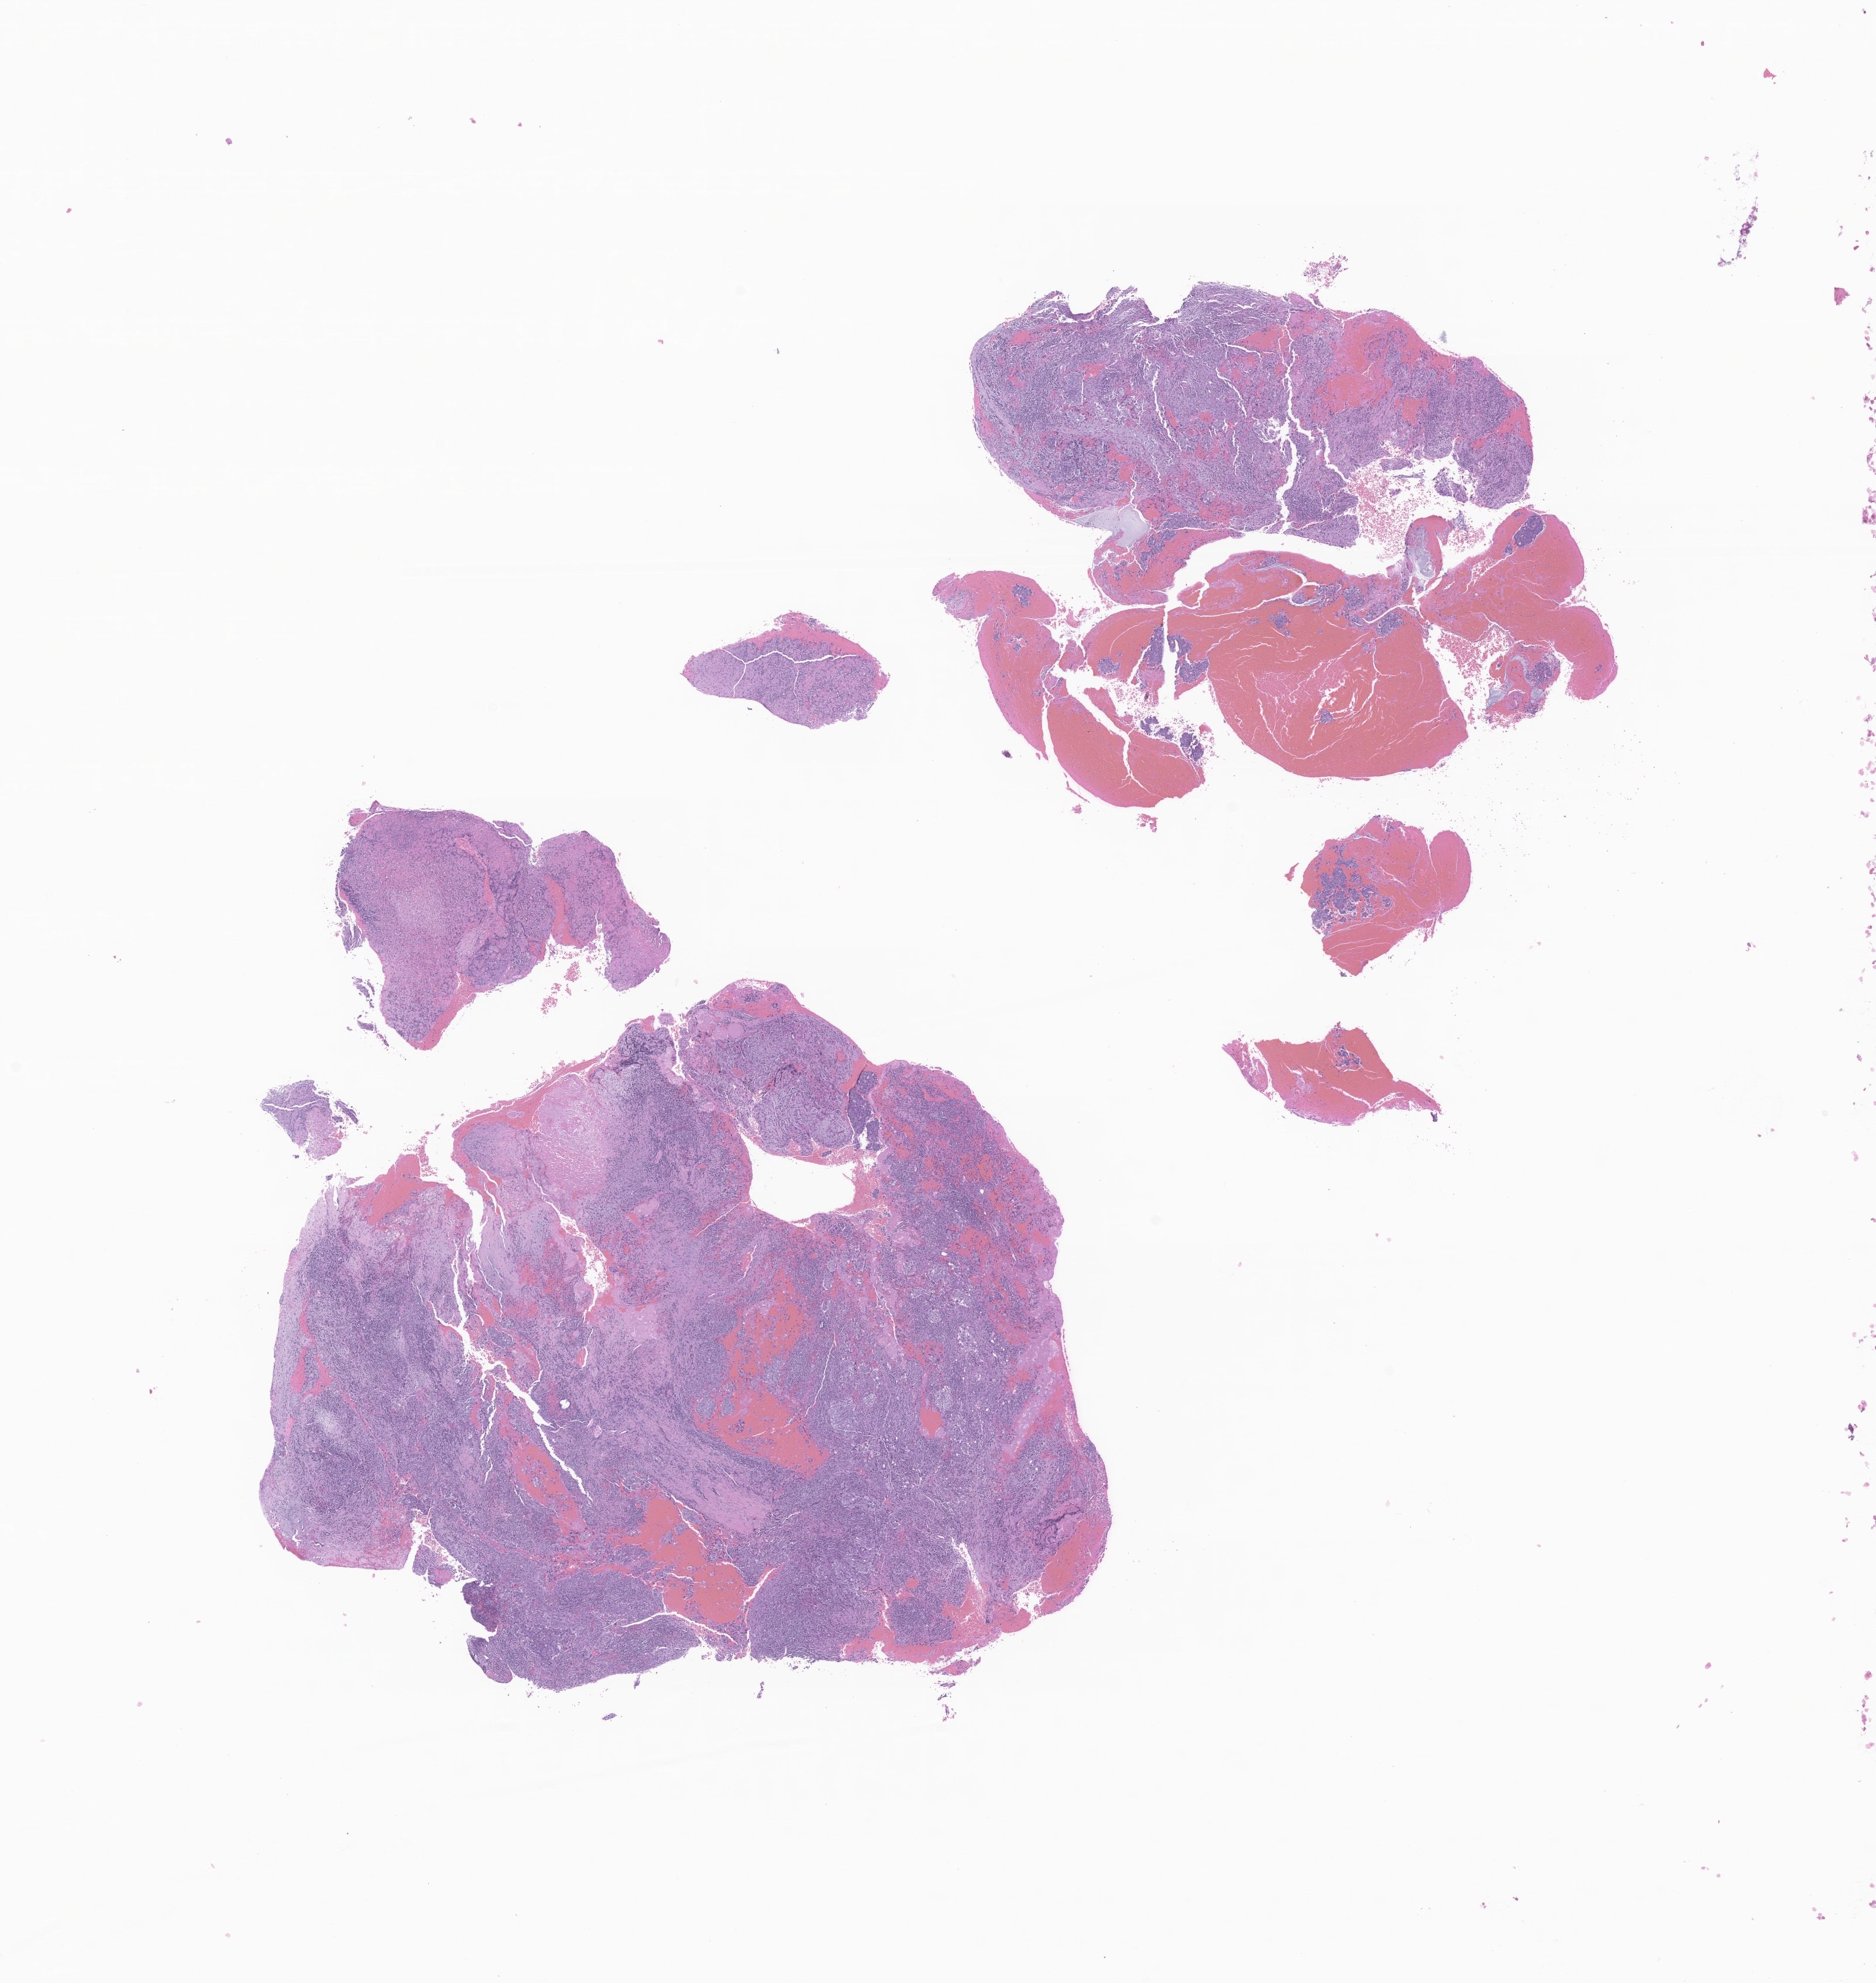
Whole-slide image, haematoxylin and eosin stain of tumor tissue from the nasopharynx — a low-resolution overview of the entire scanned area, about 13.5 x 14.3 mm. Formalin-fixed, paraffin-embedded (FFPE) tissue. Female patient, age 128 months (10 years 8 months).
Recorded diagnosis: Carcinoma, NOS.